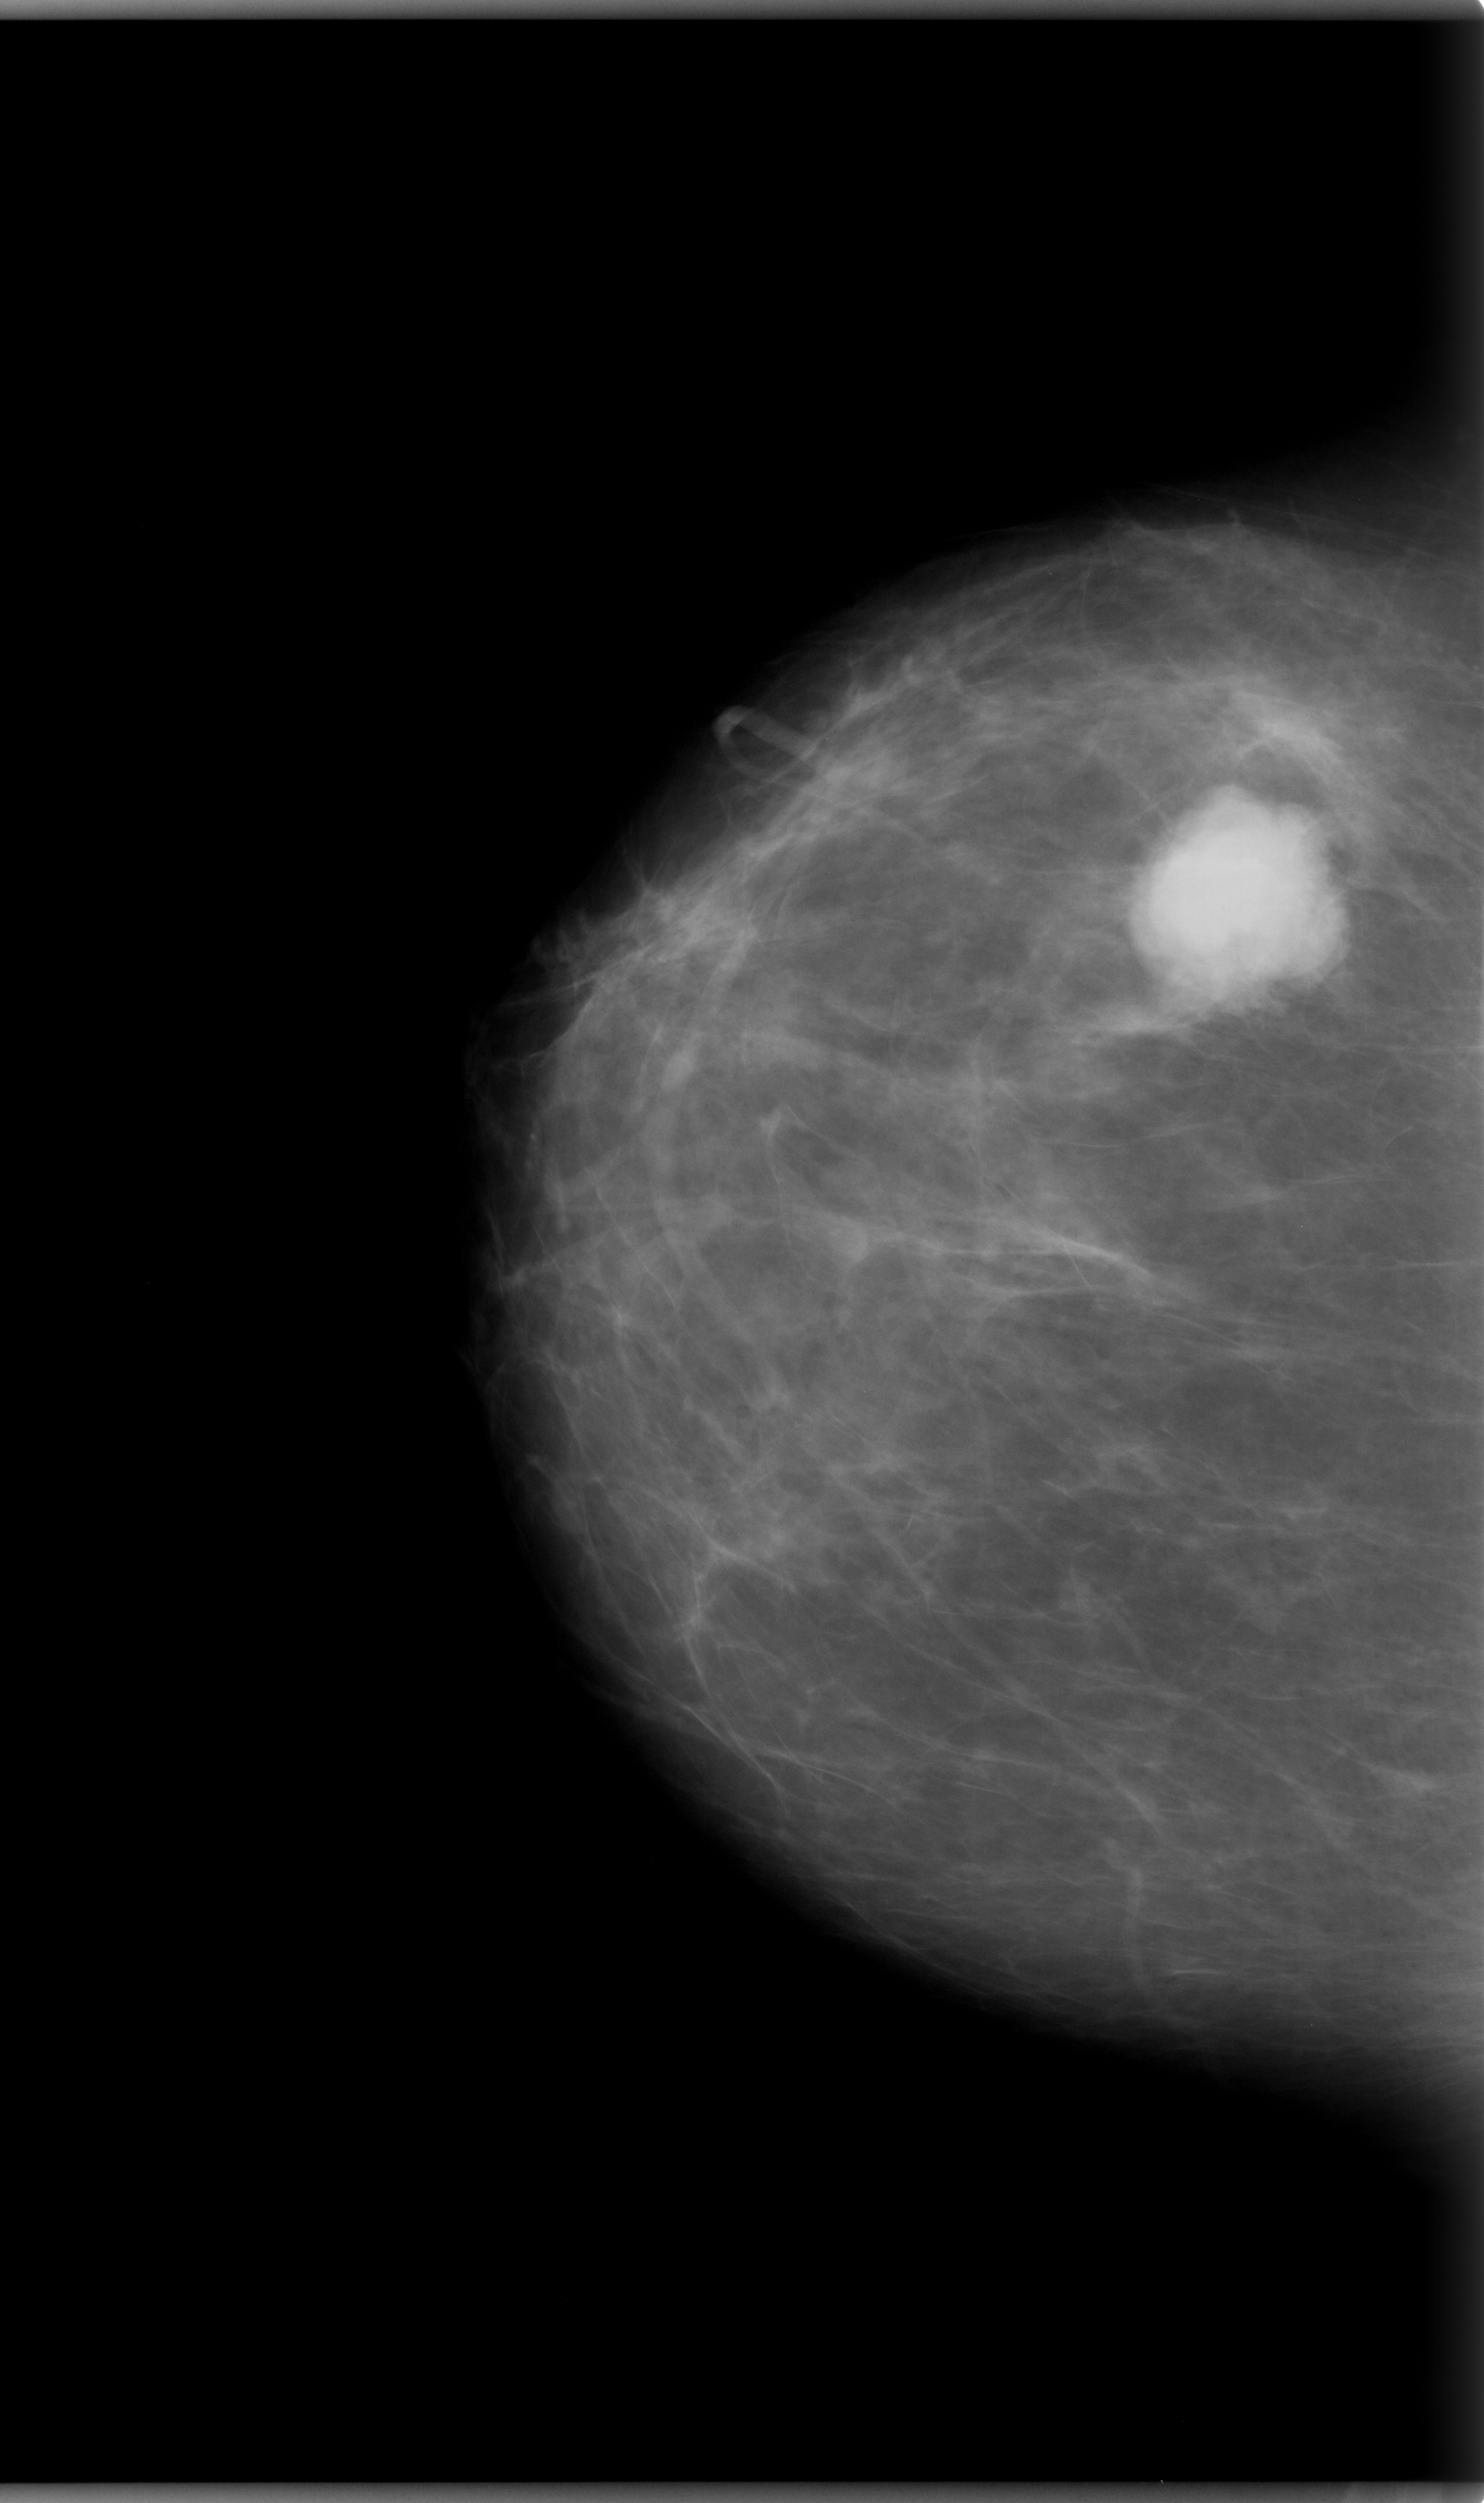
Scanned film-screen mammogram, right breast, CC view, breast composition: almost entirely fatty (BI-RADS density category 1 of 4).
Mass, shape lobulated, margins microlobulated; BI-RADS assessment category 5; pathology (as recorded): malignant.